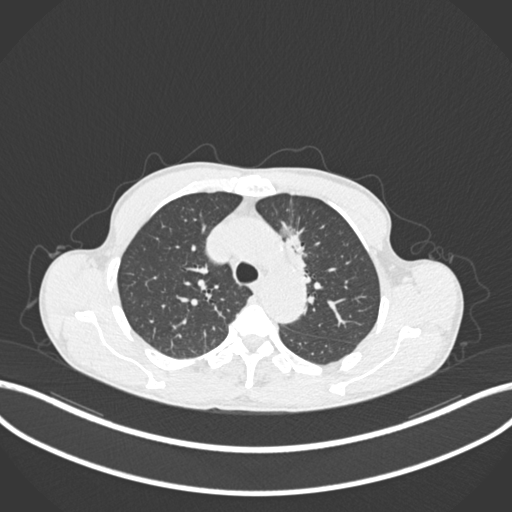
Chest CT, one axial slice; slice 144 of 211 in the series (ordered by position); lung window (W 1500 / L -600 HU); 512 × 512 image matrix, field of view 400 × 400 mm. Patient: male, 58 years. From the clinical record (not read from this slice): clinical TNM (as recorded): T1c N1 M0.
Outlined on this slice (bounding box drawn by a radiologist):
- lung tumour (recorded histology: adenocarcinoma): bounding box <281,218,311,280> (left, top, right, bottom; pixels)